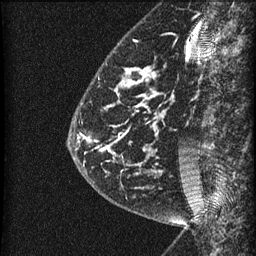
Breast MRI (dynamic contrast-enhanced), one sagittal slice. Position 16 of 60 along the scan axis. Dynamic contrast-enhanced series, image 2 of 3 at this slice position (ordered by acquisition). 1.5 T. TE 4.2 ms, TR 22.7 ms. 1.5 mm slice thickness. 256 × 256 image matrix. Female patient, age 48 years. Case-level facts recorded for this patient, not image findings: setting: breast cancer imaged before/during neoadjuvant chemotherapy; receptor status: triple-negative.
Structures marked on this image (semi-automatic segmentation, software-assisted and operator-edited):
- analysis volume of interest (the breast-tissue region the enhancement analysis was run in; not a lesion): bounding box (x1, y1, x2, y2) in pixels: (81, 23, 186, 202)
- tumour enhancement mask (voxels above the 90 % enhancement threshold inside the analysis volume of interest): (81, 68, 154, 155)